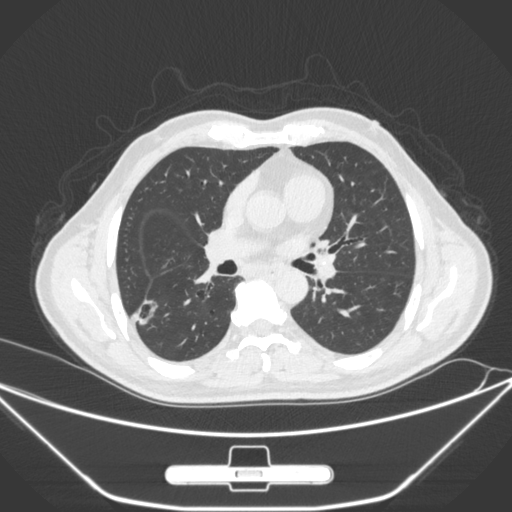
Chest CT, one axial slice; position 155 of 310 along the scan axis; lung window (W 1500 / L -600 HU); 1 mm slice thickness; 512 × 512 image matrix. Male patient, age 71 years. Case-level facts recorded for this patient, not image findings: clinical TNM (as recorded): T1c N0 M0; histopathological grade: G2.
Outlined on this slice (bounding box drawn by a radiologist):
- lung tumour (recorded histology: adenocarcinoma): box from (x=133, y=295) to (x=161, y=336) px